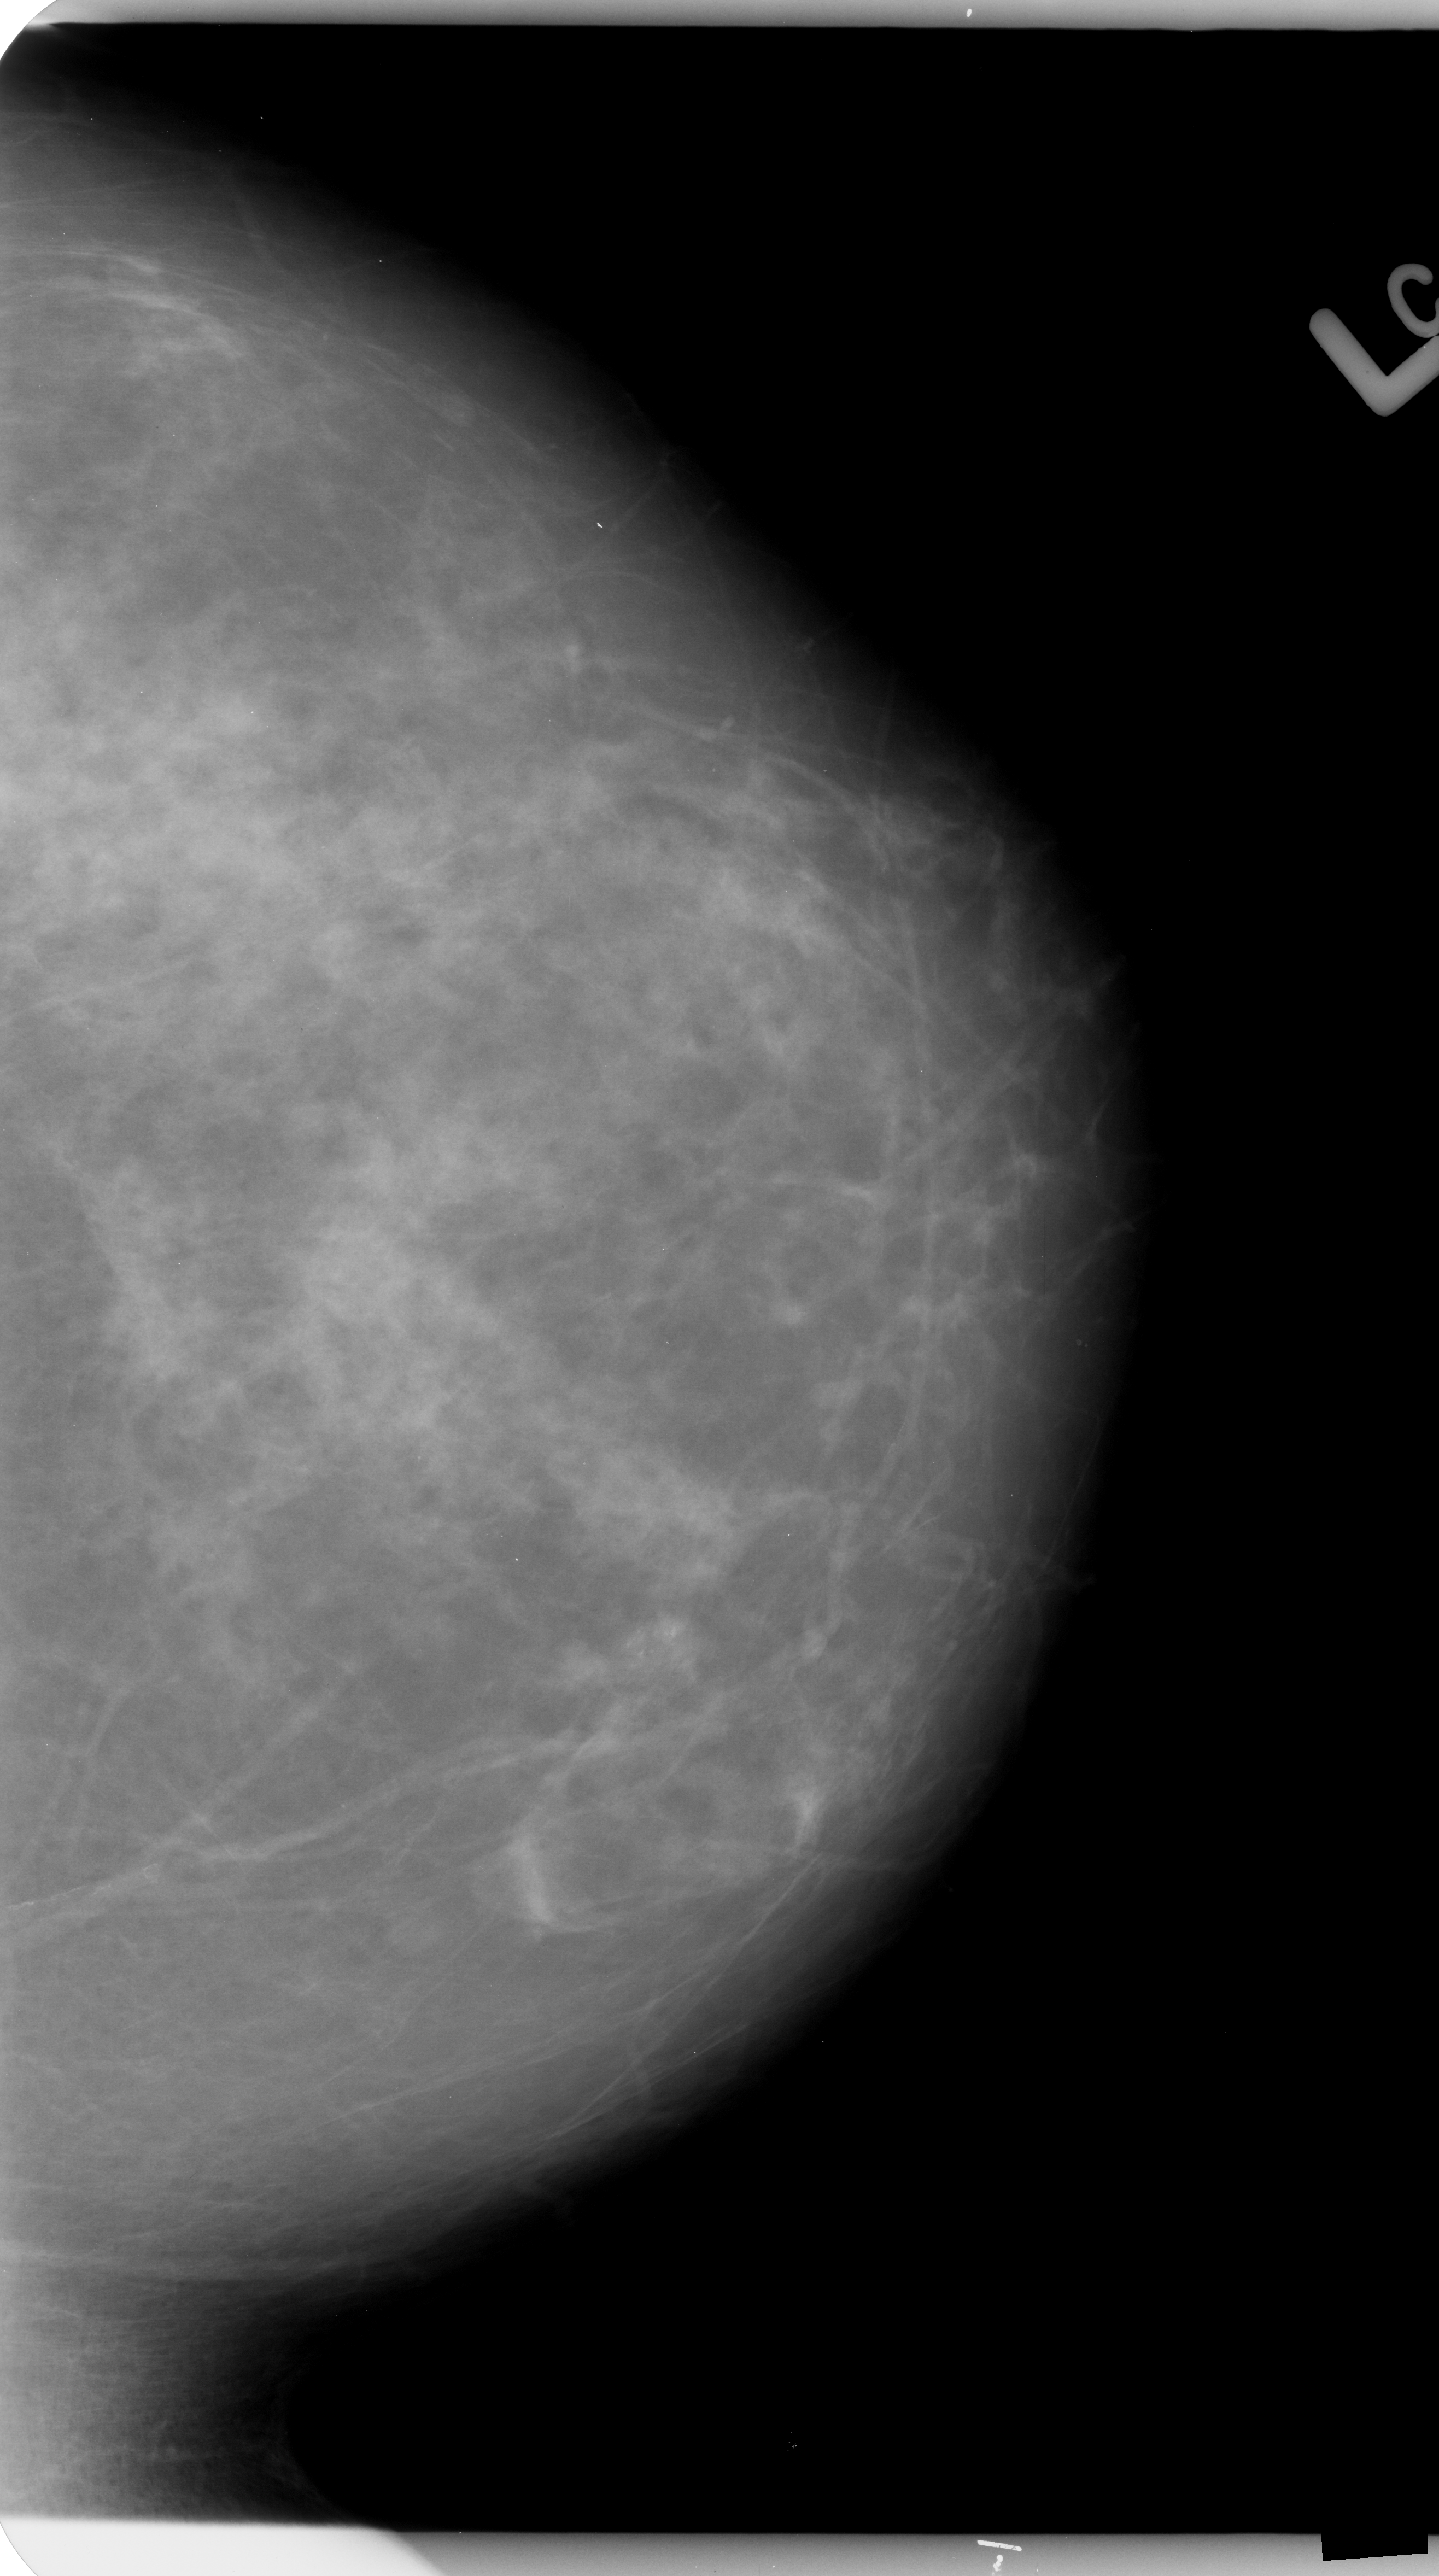
Digitized screen-film mammogram; left breast; CC view; breast composition: scattered fibroglandular densities (BI-RADS density category 2 of 4).
- Calcifications, morphology pleomorphic, distribution clustered; BI-RADS assessment category 4; subtlety rating 3 on a 1 (subtle) to 5 (obvious) scale; pathology result (as recorded, not read from the image): benign.